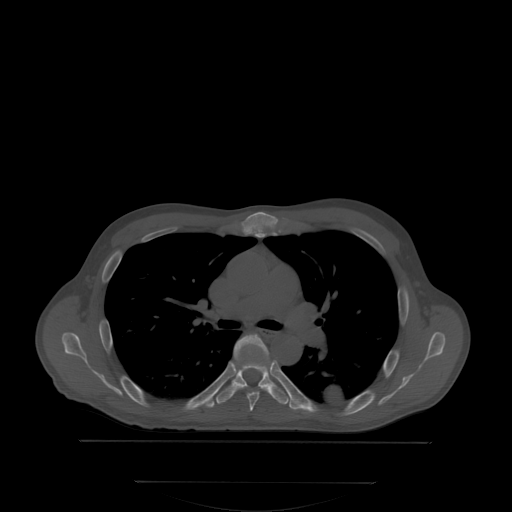
CT including the spine, one axial slice. Bone window (W 1800 / L 400 HU). 2.5 mm slice thickness. 512 × 512 image matrix, field of view 500 × 500 mm. Patient: male, 58 years. From the clinical record (not read from this slice): primary cancer: prostate; vertebrae with lytic lesions (as recorded): L1.
Annotated regions visible in this slice (semi-automatic segmentation, software-assisted and operator-edited):
- T5 vertebra: bounding box <236,335,269,411> (left, top, right, bottom; pixels)
- T6 vertebra: <203,336,302,404>